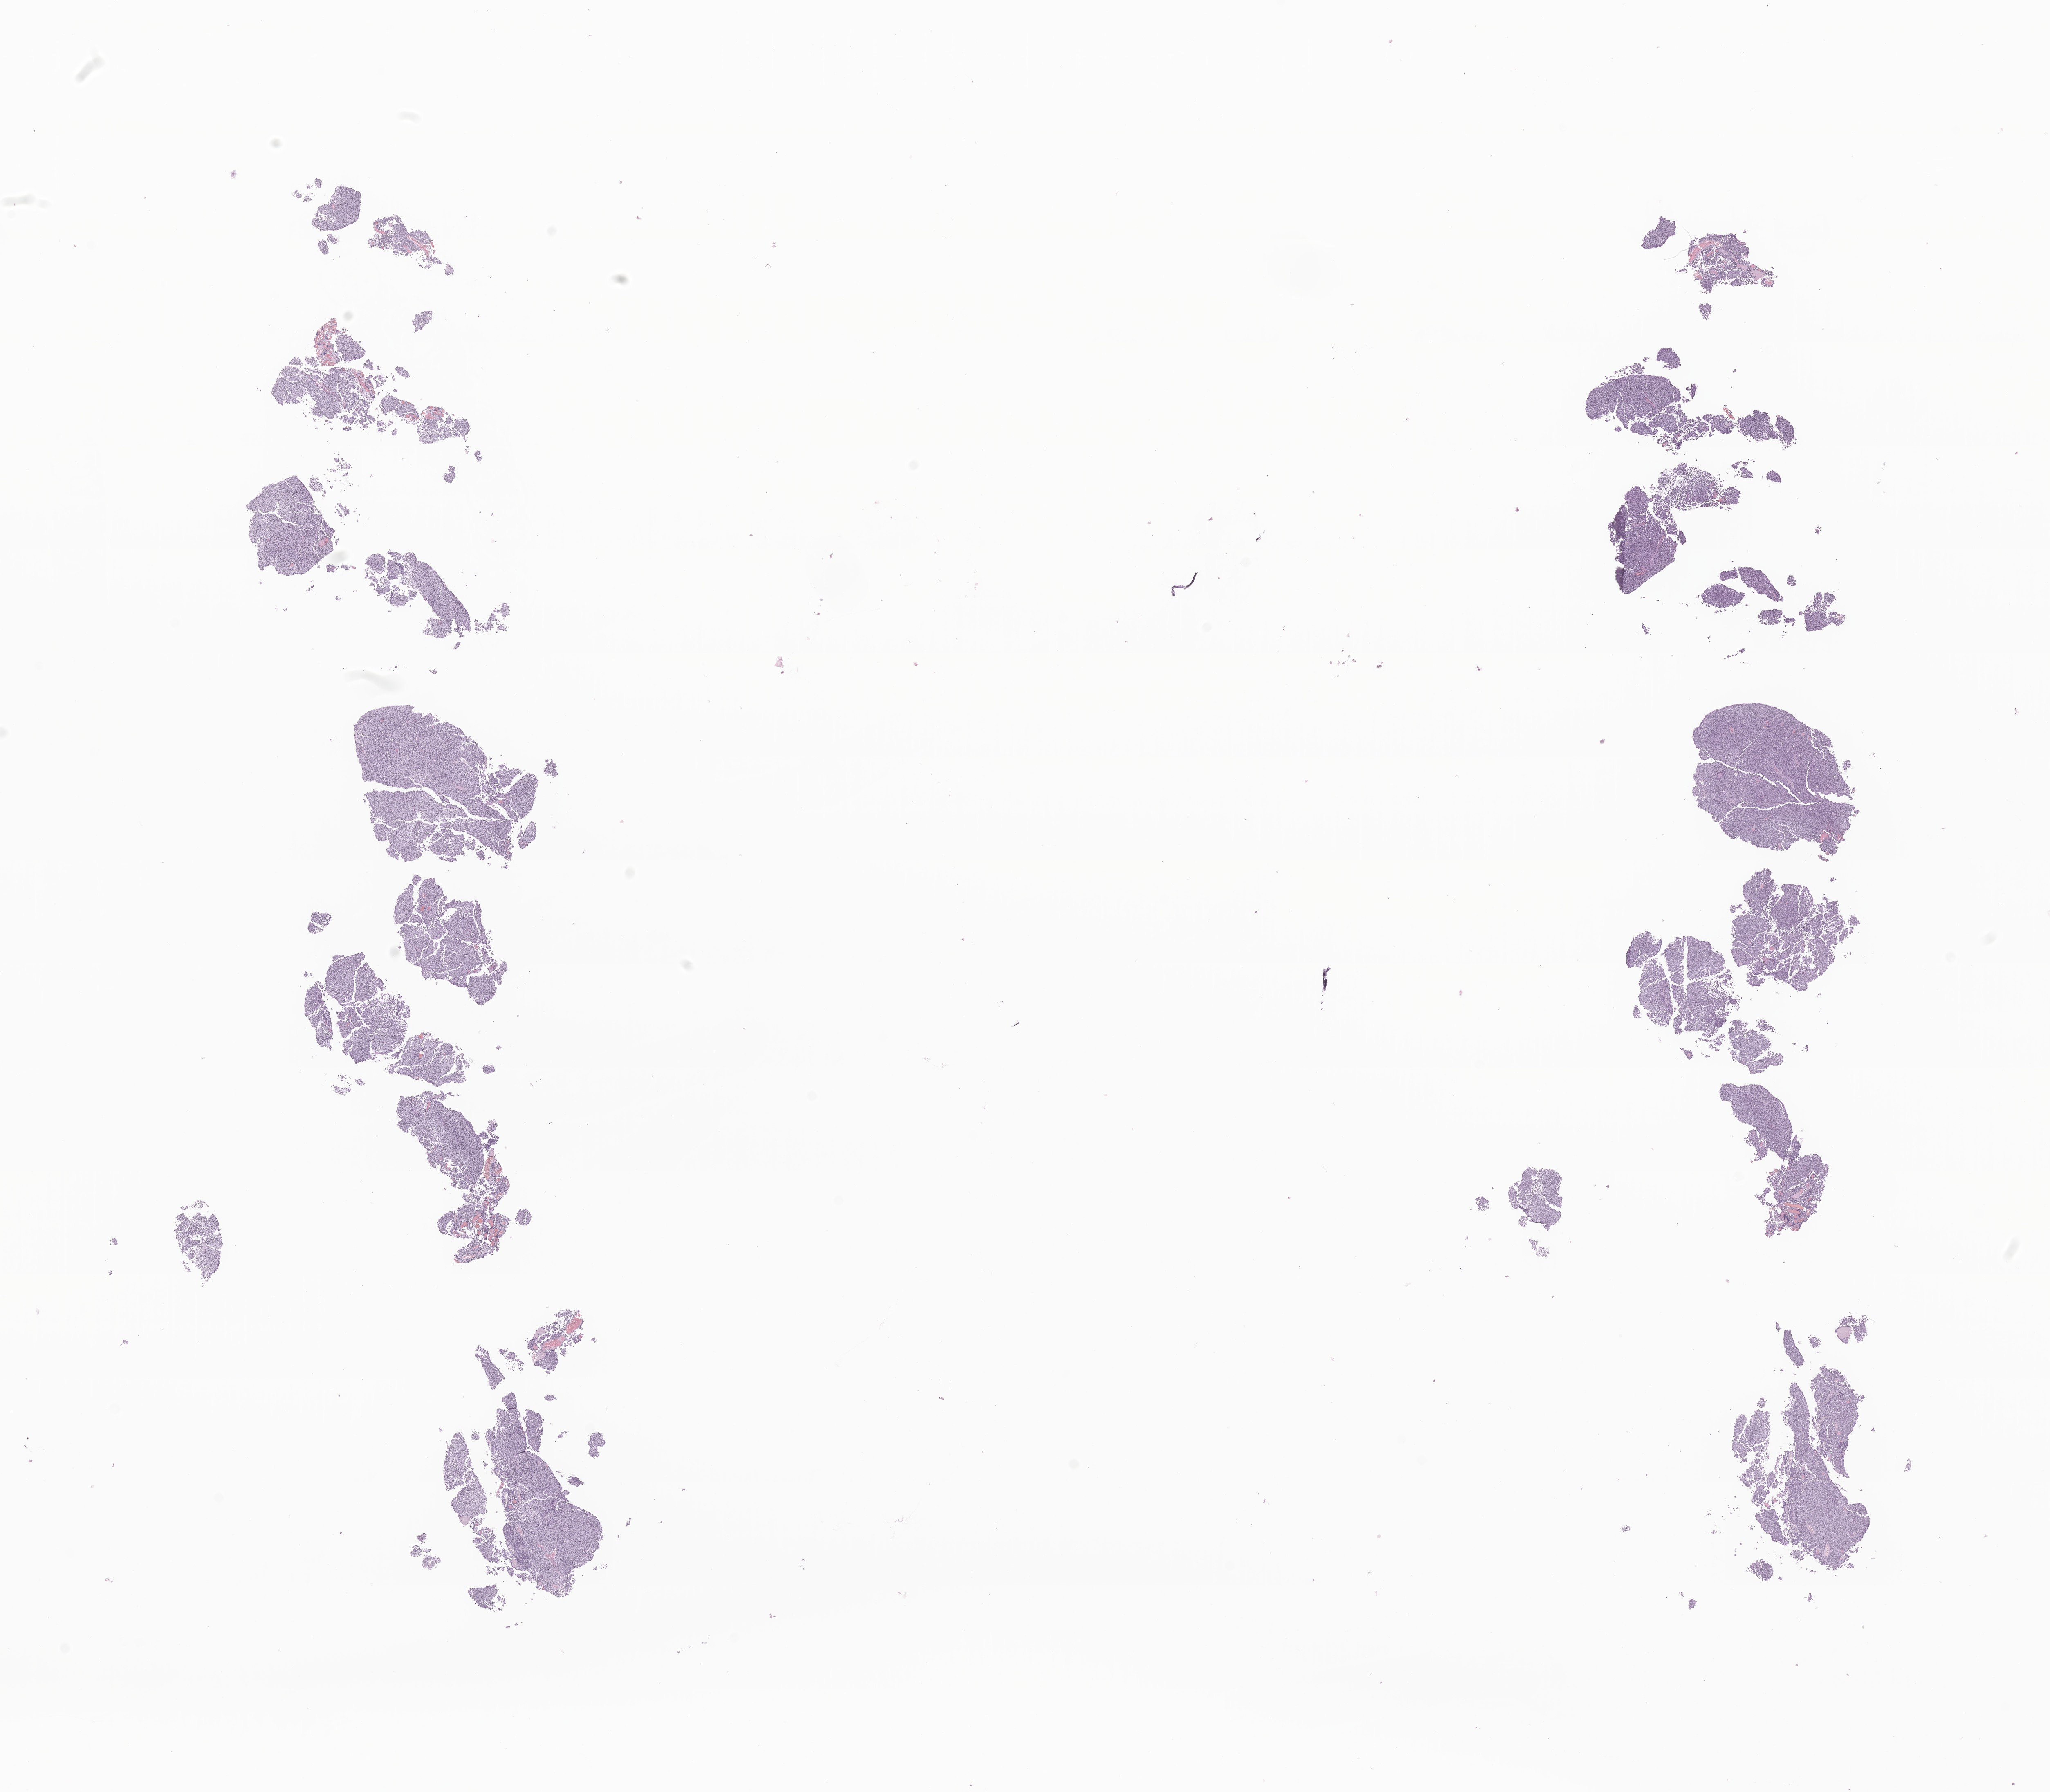
H&E whole-slide image of tumor tissue from the brain, a low-resolution overview of the entire scanned area, about 21.1 x 18.5 mm, formalin-fixed, paraffin-embedded (FFPE) tissue. Patient female; age 136 months (11 years 4 months).
Diagnosis (ICD-O-3 morphology term): Pineoblastoma.